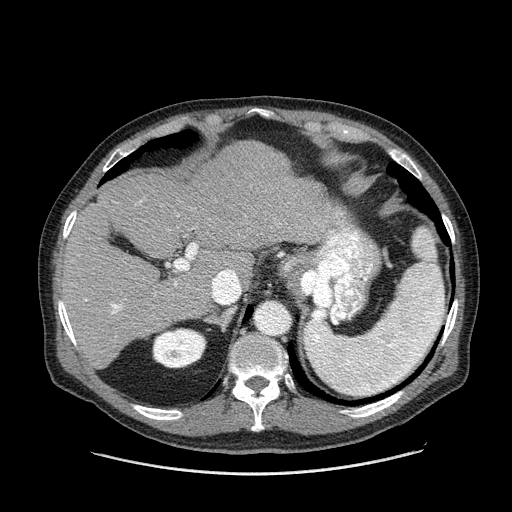
Contrast-enhanced abdominal CT (liver protocol), one axial slice; slice 102 of 180 in the series (ordered by position); reconstruction kernel STANDARD; one of 2 acquisitions stored at this slice position; soft-tissue window (W 400 / L 40 HU); 2.5 mm slice thickness; 512 × 512 image matrix, field of view 420 × 420 mm. From the clinical record (not read from this slice): diagnosis: hepatocellular carcinoma (patient treated with transarterial chemoembolisation; whether this scan precedes or follows treatment is not stated here); TNM stage (as recorded): Stage-II; Child-Pugh class: A; tumour nodularity: multinodular; tumour size: 2.8 cm.
Annotated regions visible in this slice (semi-automatically segmented with operator editing):
- liver parenchyma outside the tumour (the mass and vessels are separate outlines, so this box may not span the whole liver): bounding box [x1, y1, x2, y2] px = [60, 140, 348, 368]
- liver vessels: [72, 201, 180, 344]